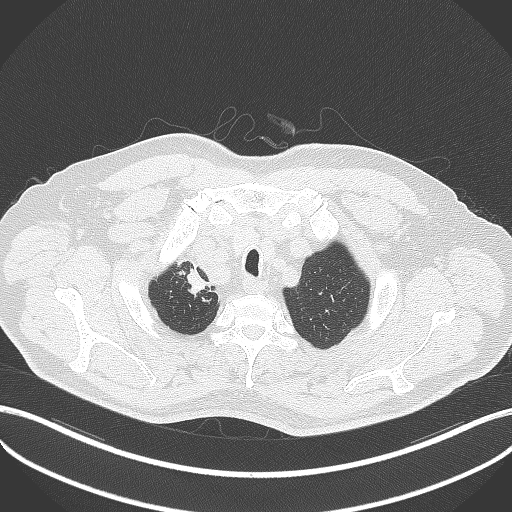
Chest CT, one axial slice. Position 345 of 411 along the scan axis. 120 kVp. Lung window (W 1500 / L -600 HU). 1 mm slice thickness. 512 × 512 image matrix, field of view 400 × 400 mm. Patient: male, 60 years. From the clinical record (not read from this slice): clinical TNM (as recorded): T1b N1 M0.
Structures marked on this image (rectangle marked by the reading radiologist):
- lung tumour (recorded histology: squamous cell carcinoma): box from (x=182, y=268) to (x=208, y=296) px